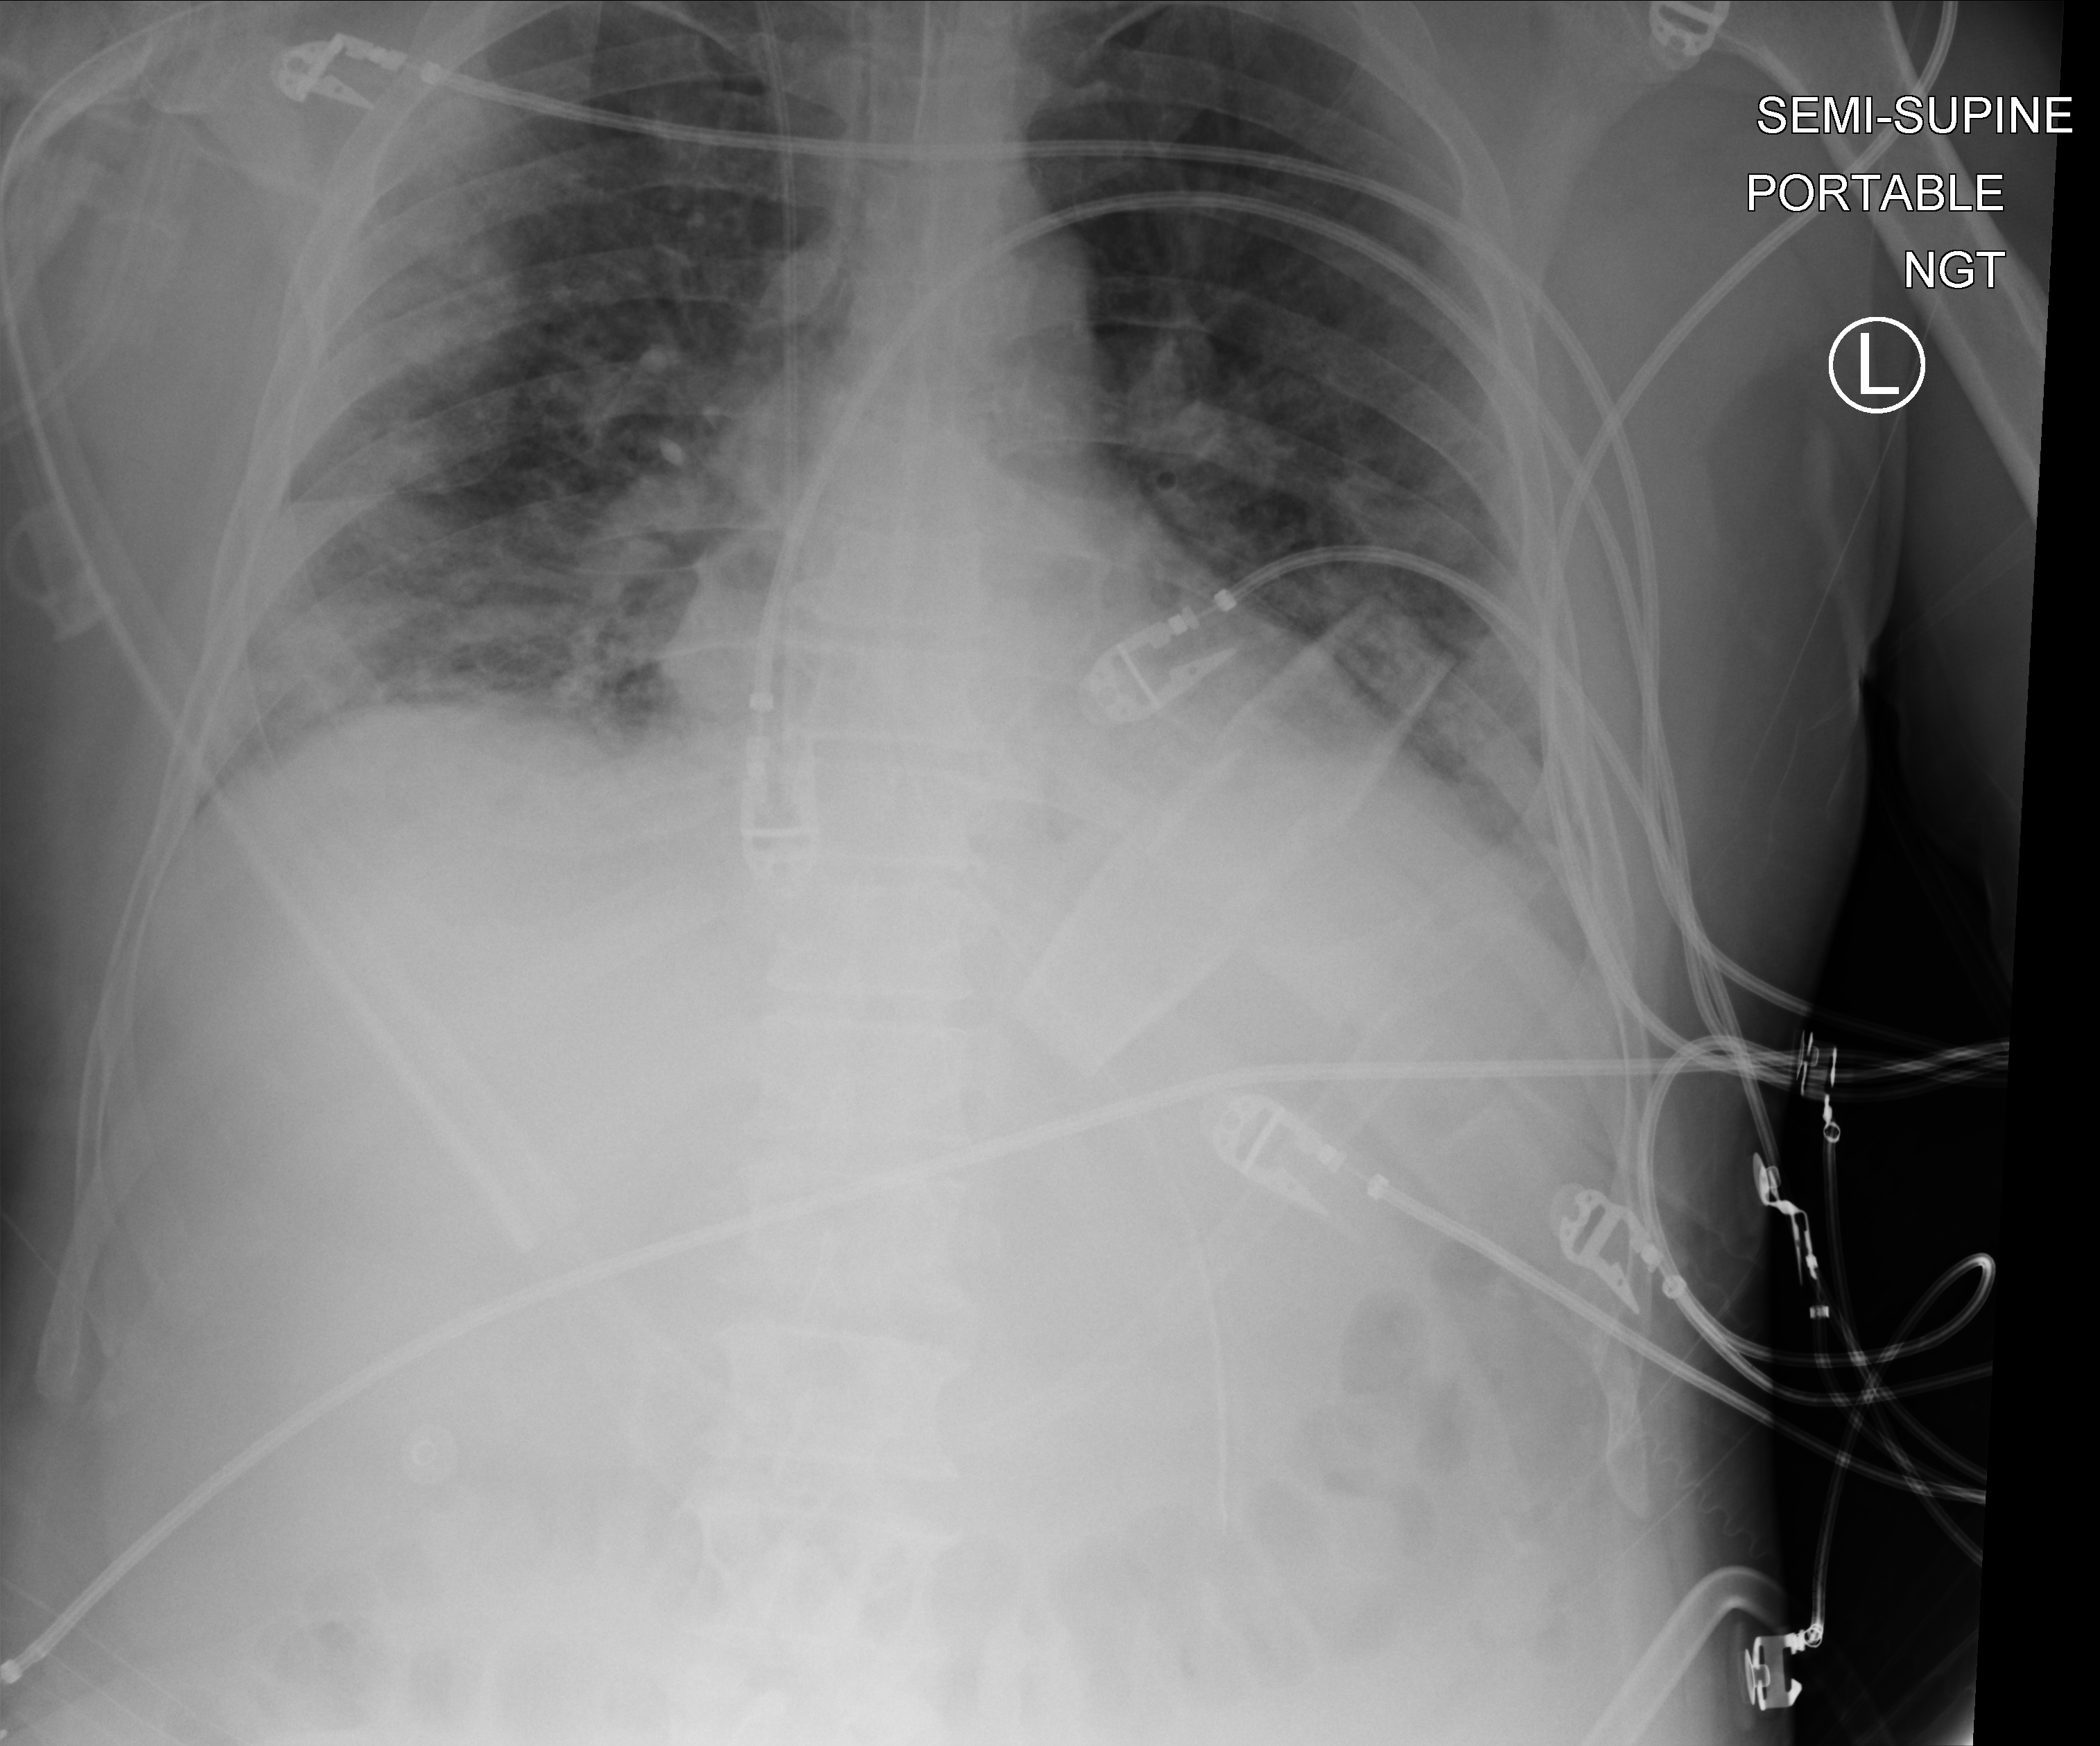
Portable chest radiograph. Male patient hospitalised with COVID-19, age 18–59 years.
Hospital-stay facts (about this admission, not read from this image; timing relative to this image not recorded): mechanically ventilated during this hospital stay: yes; COPD (admission record): no; admitted to intensive care during this hospital stay: yes.